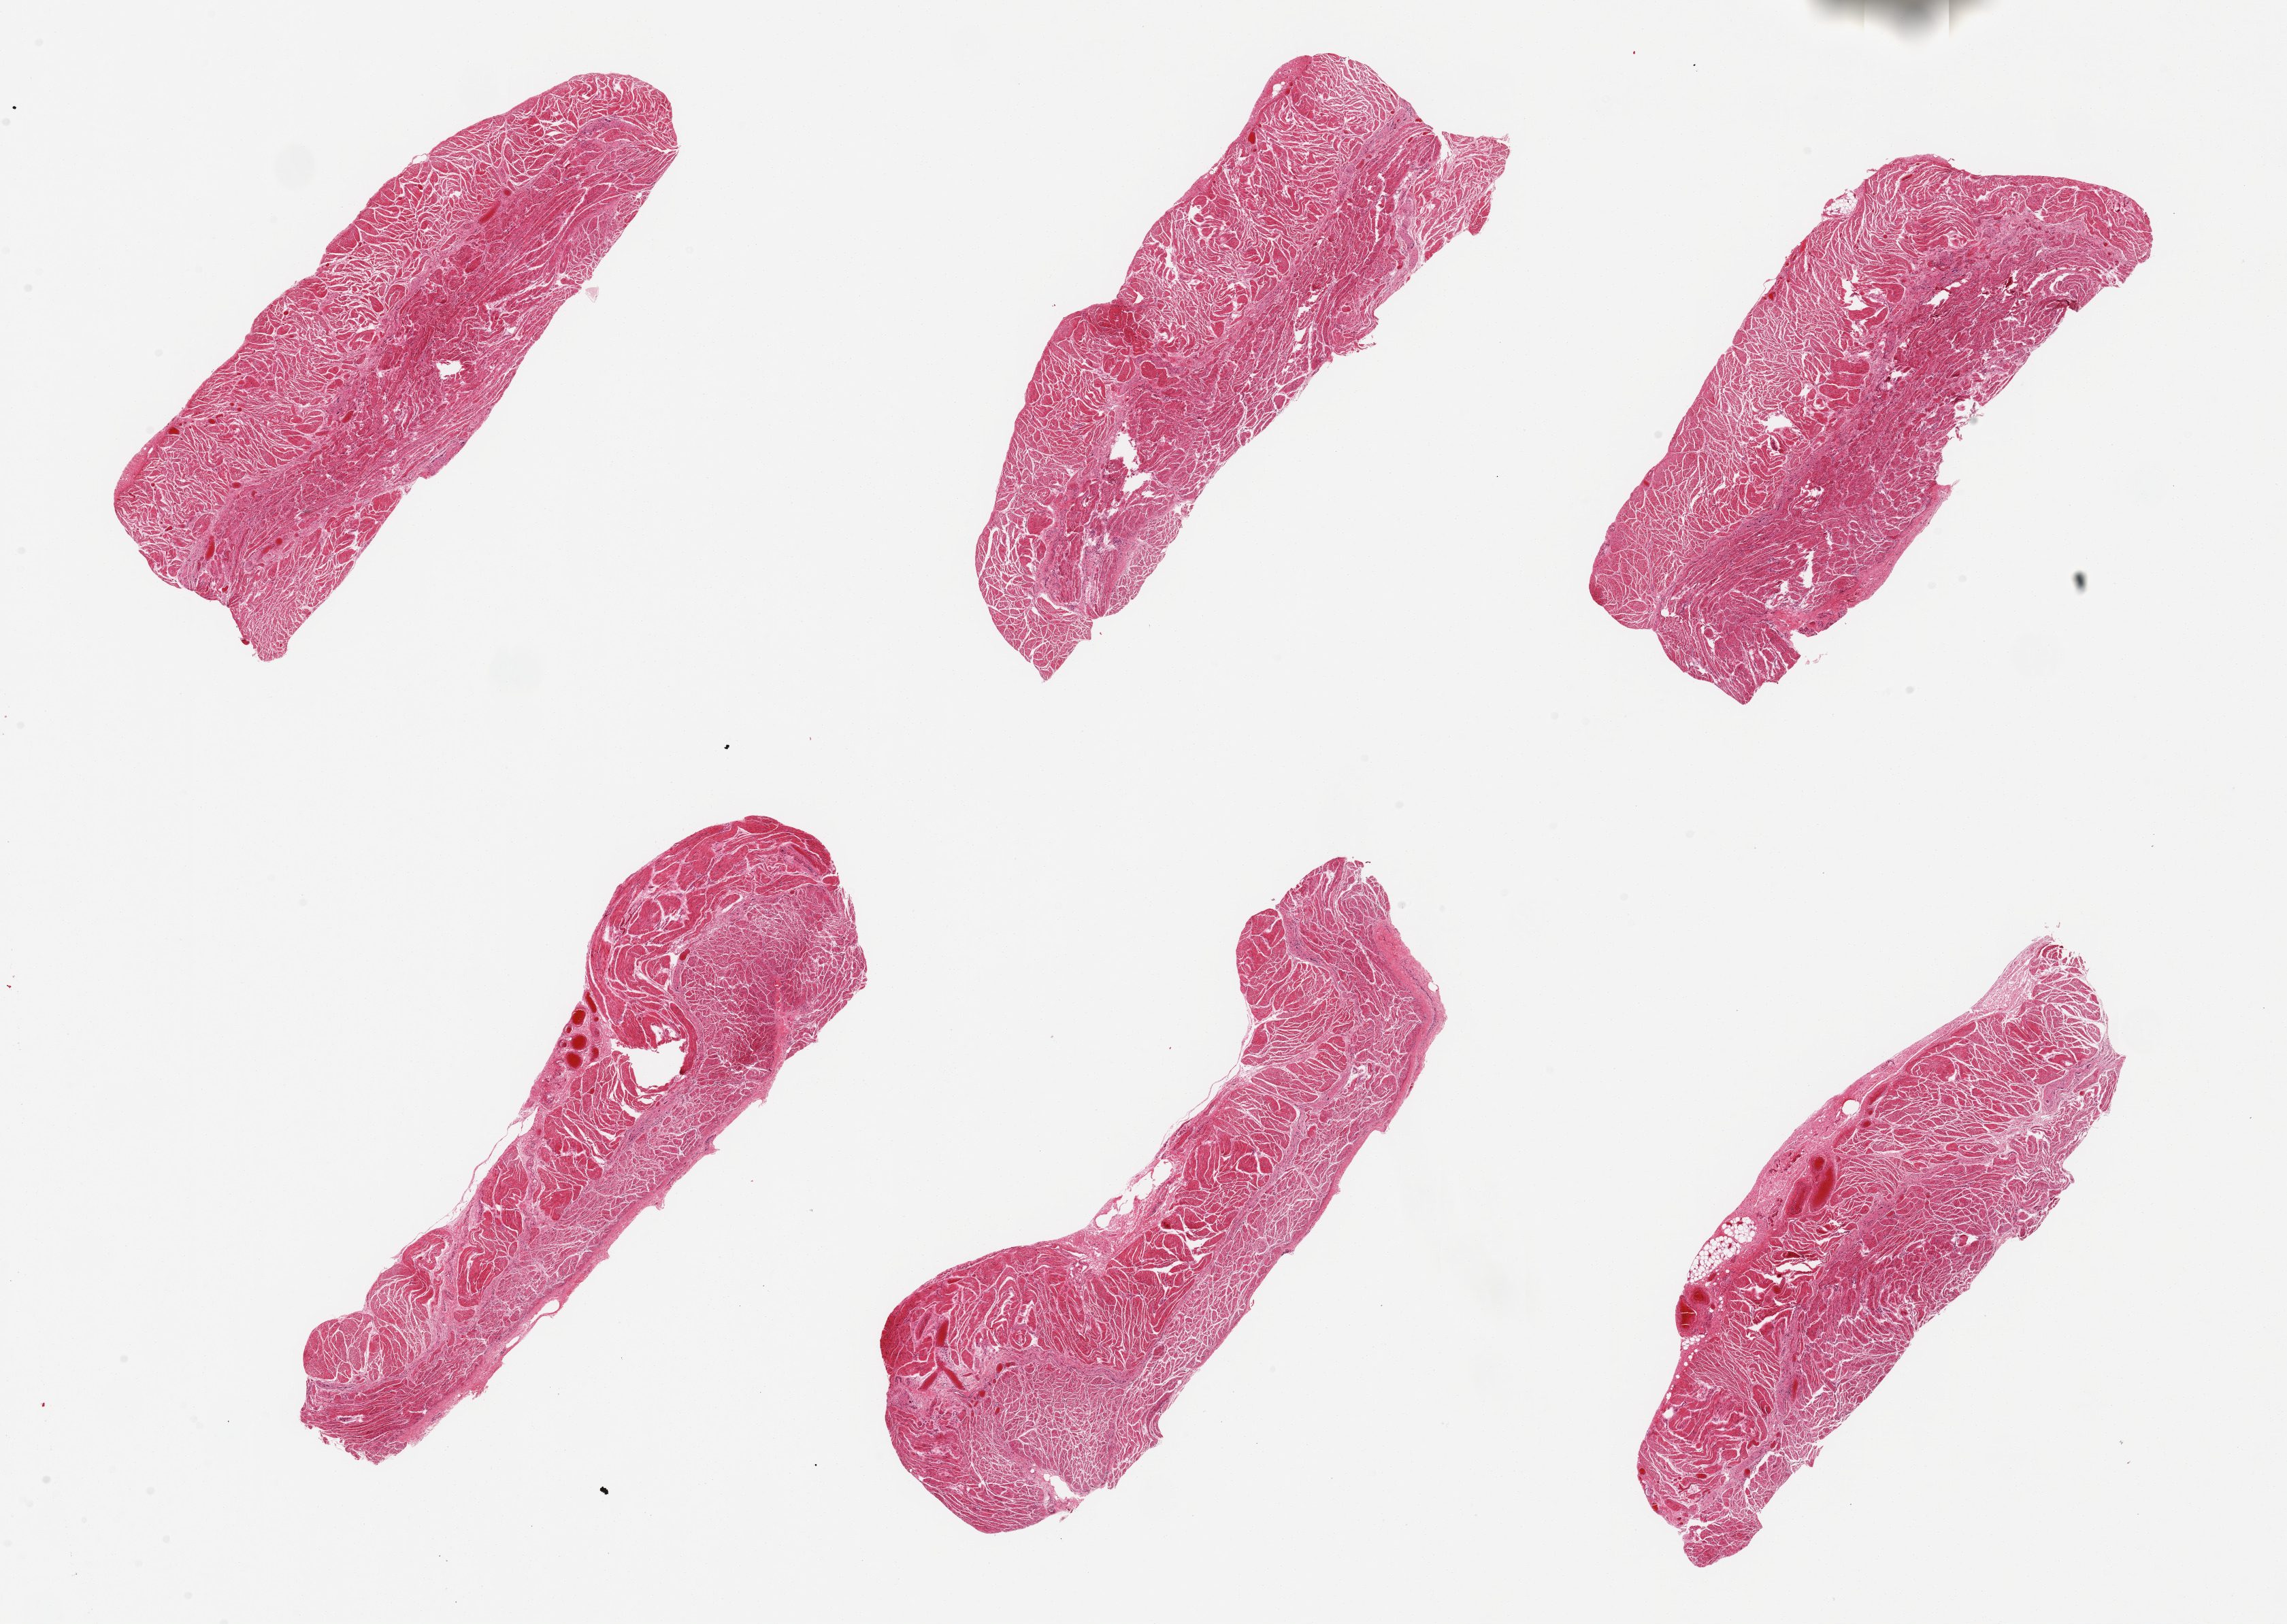
Digitized H&E-stained section, whole scanned area (about 26.6 x 18.9 mm, acquisition: 20x scan) shown as a low-resolution overview. PAXgene-fixed paraffin-embedded (PFPE) section. Sampled site (target tissue): esophageal muscle. Donor tissue sample.
Pathologist's review note for this sample: 6 pieces; well dissected muscle layer.